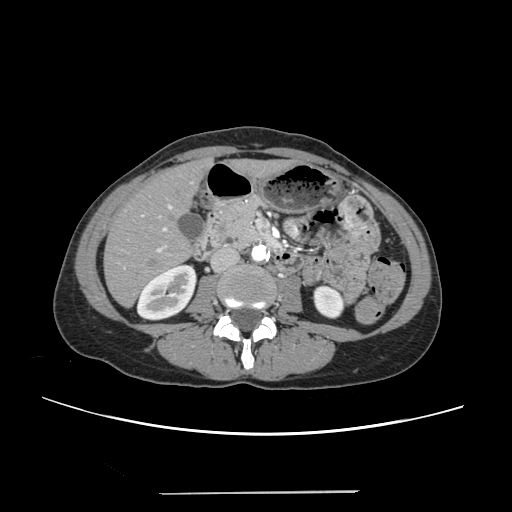
Contrast-enhanced abdominal CT, one axial slice; slice 87 of 240 in the series (ordered by position); soft-tissue window (W 400 / L 40 HU); 512 × 512 image matrix, field of view 371 × 371 mm. Female patient, age 60 years. From the clinical record (not read from this slice): diagnosis: colorectal cancer liver metastases, imaged before liver resection; multiple liver metastases: no; largest metastasis: 1.5 cm.
Outlined on this slice (manually delineated by an expert):
- liver: bounding box <105,163,282,305> (left, top, right, bottom; pixels)
- planned liver remnant (the part of the liver to remain after resection): <105,163,281,305>
- portal vein (with intrahepatic branches): <123,205,172,268>